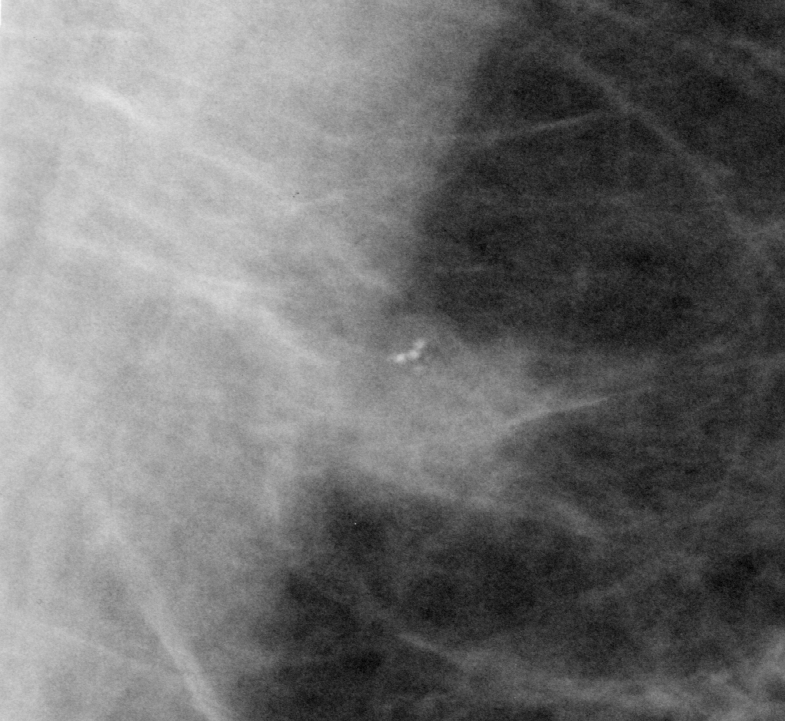
Region of interest cut from a scanned film mammogram (one marked finding); left breast; MLO view; BI-RADS breast density category 2 (scale 1–4).
- Marked abnormality: calcifications, morphology pleomorphic, distribution clustered; BI-RADS assessment category 5; subtlety rating 5 on a 1 (subtle) to 5 (obvious) scale; pathology result (as recorded, not read from the image): malignant.